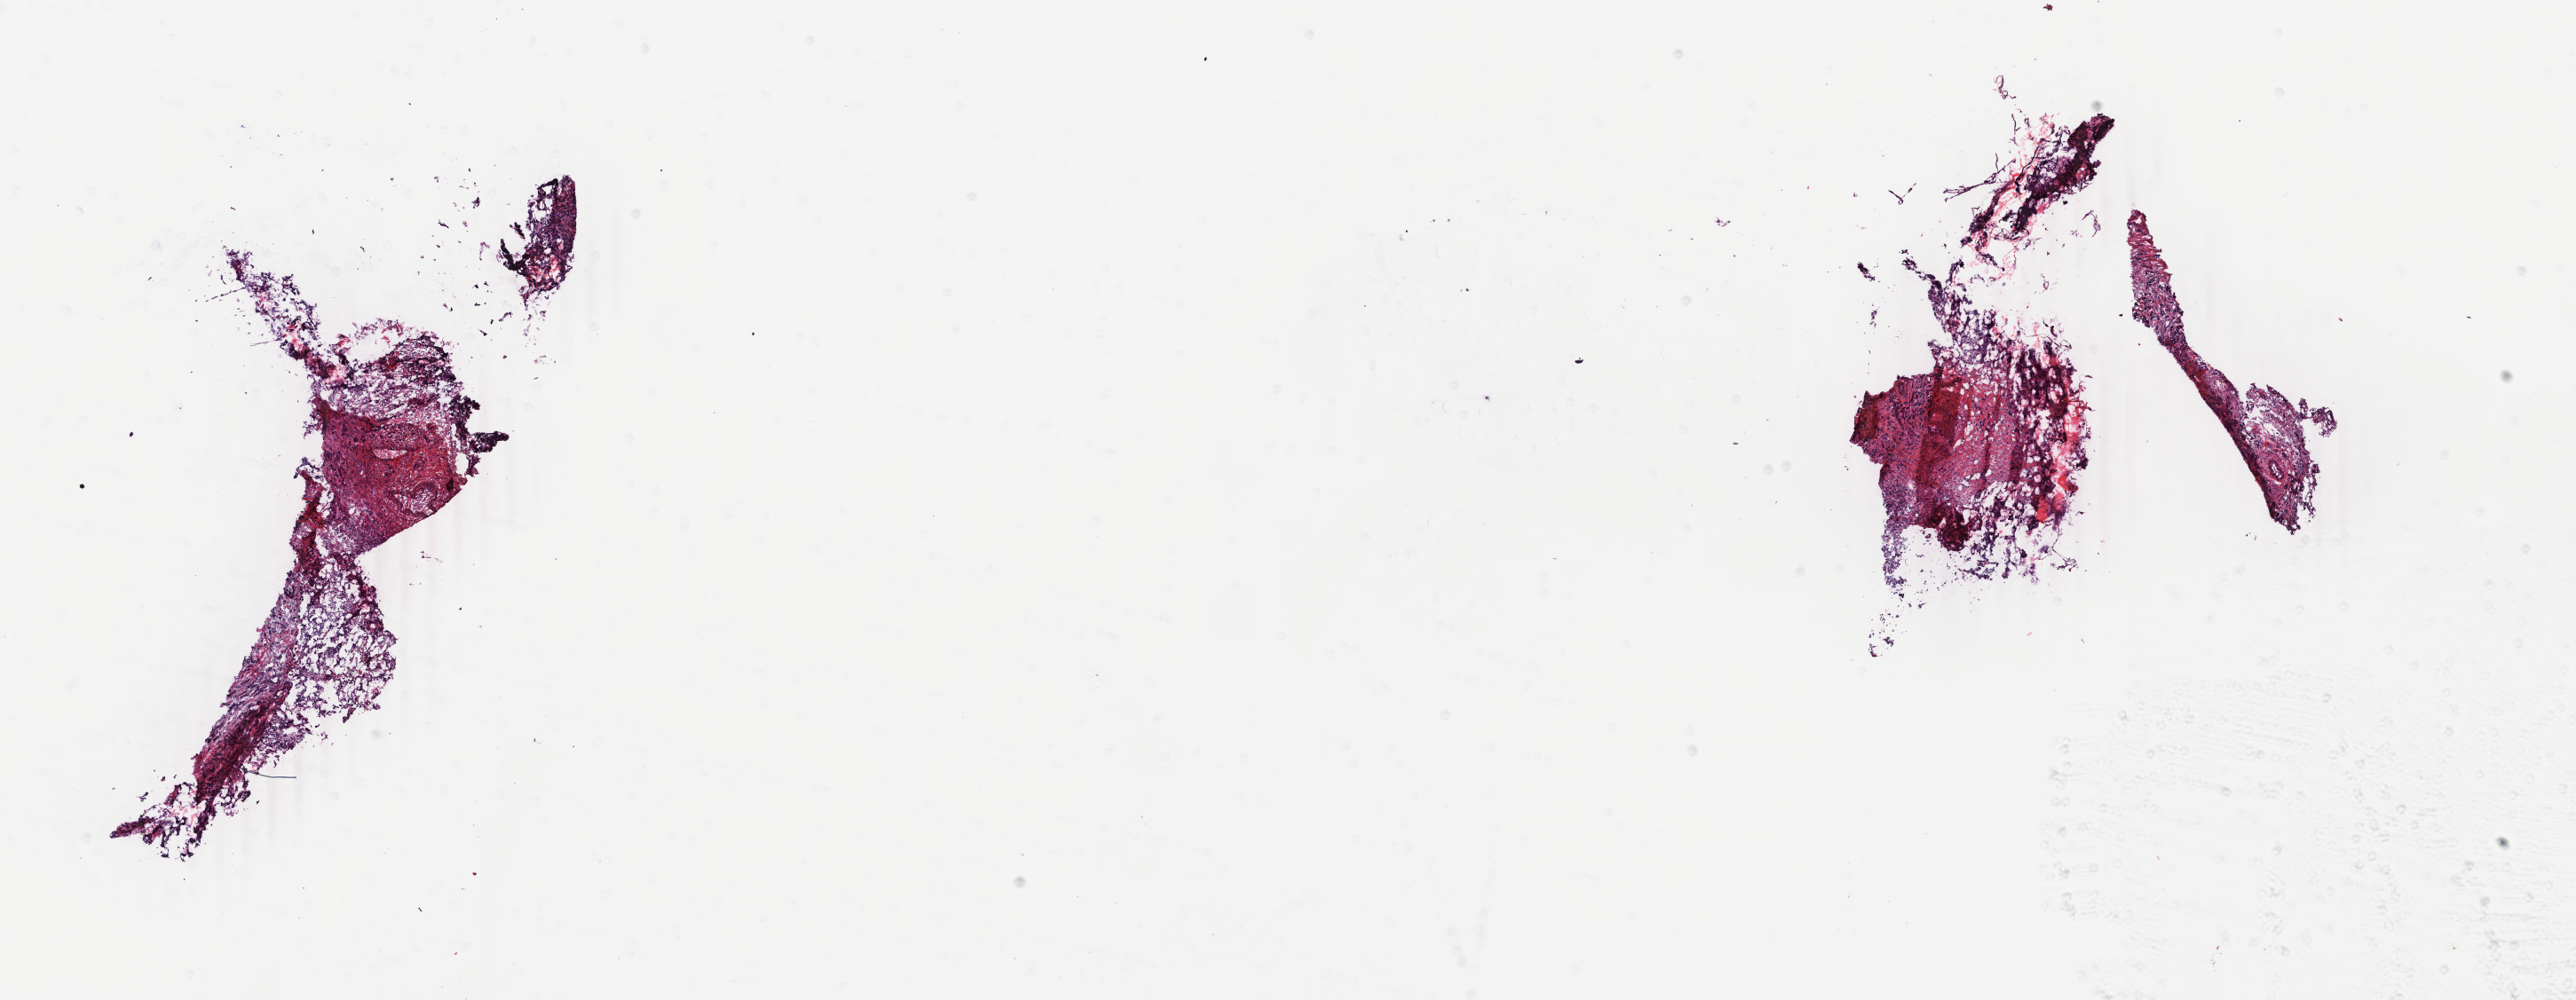
H&E-stained whole-slide image, low-resolution overview of the scanned area, about 23.1 x 9.0 mm; frozen section from the bottom of the tissue portion; primary tumour sample from the breast. Female patient; age at initial diagnosis 61 years. Composition of this section per pathologist review: tumour cells 85%, tumour nuclei 85%, normal cells 0%, stromal cells 15%, necrosis 0%. Inflammatory infiltration, as recorded: lymphocyte infiltration 1%, monocyte infiltration 0%, neutrophil infiltration 0%.
TNM: T2 N3 M0. Histologic diagnosis: Lobular carcinoma, NOS. AJCC pathologic stage: IIIC.